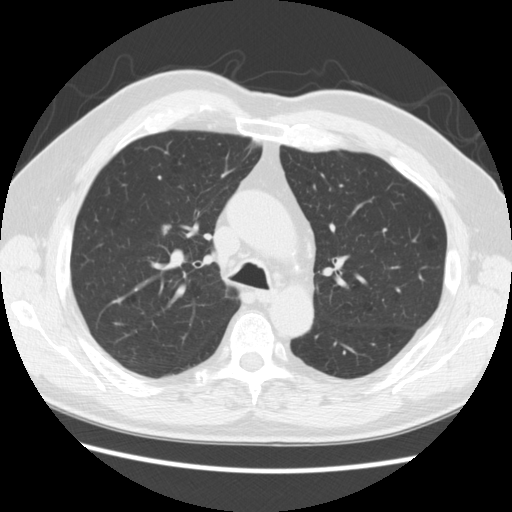
Low-dose screening chest CT, one axial slice; slice 174 of 259 in the series (ordered by position); reconstruction kernel STANDARD; lung window (W 1500 / L -600 HU); 512 × 512 image matrix, field of view 360 × 360 mm.
Structures marked on this image (manually delineated by an expert):
- lesion 1 (tumor, upper lobe of right lung): bounding box <163,225,171,235> (left, top, right, bottom; pixels)